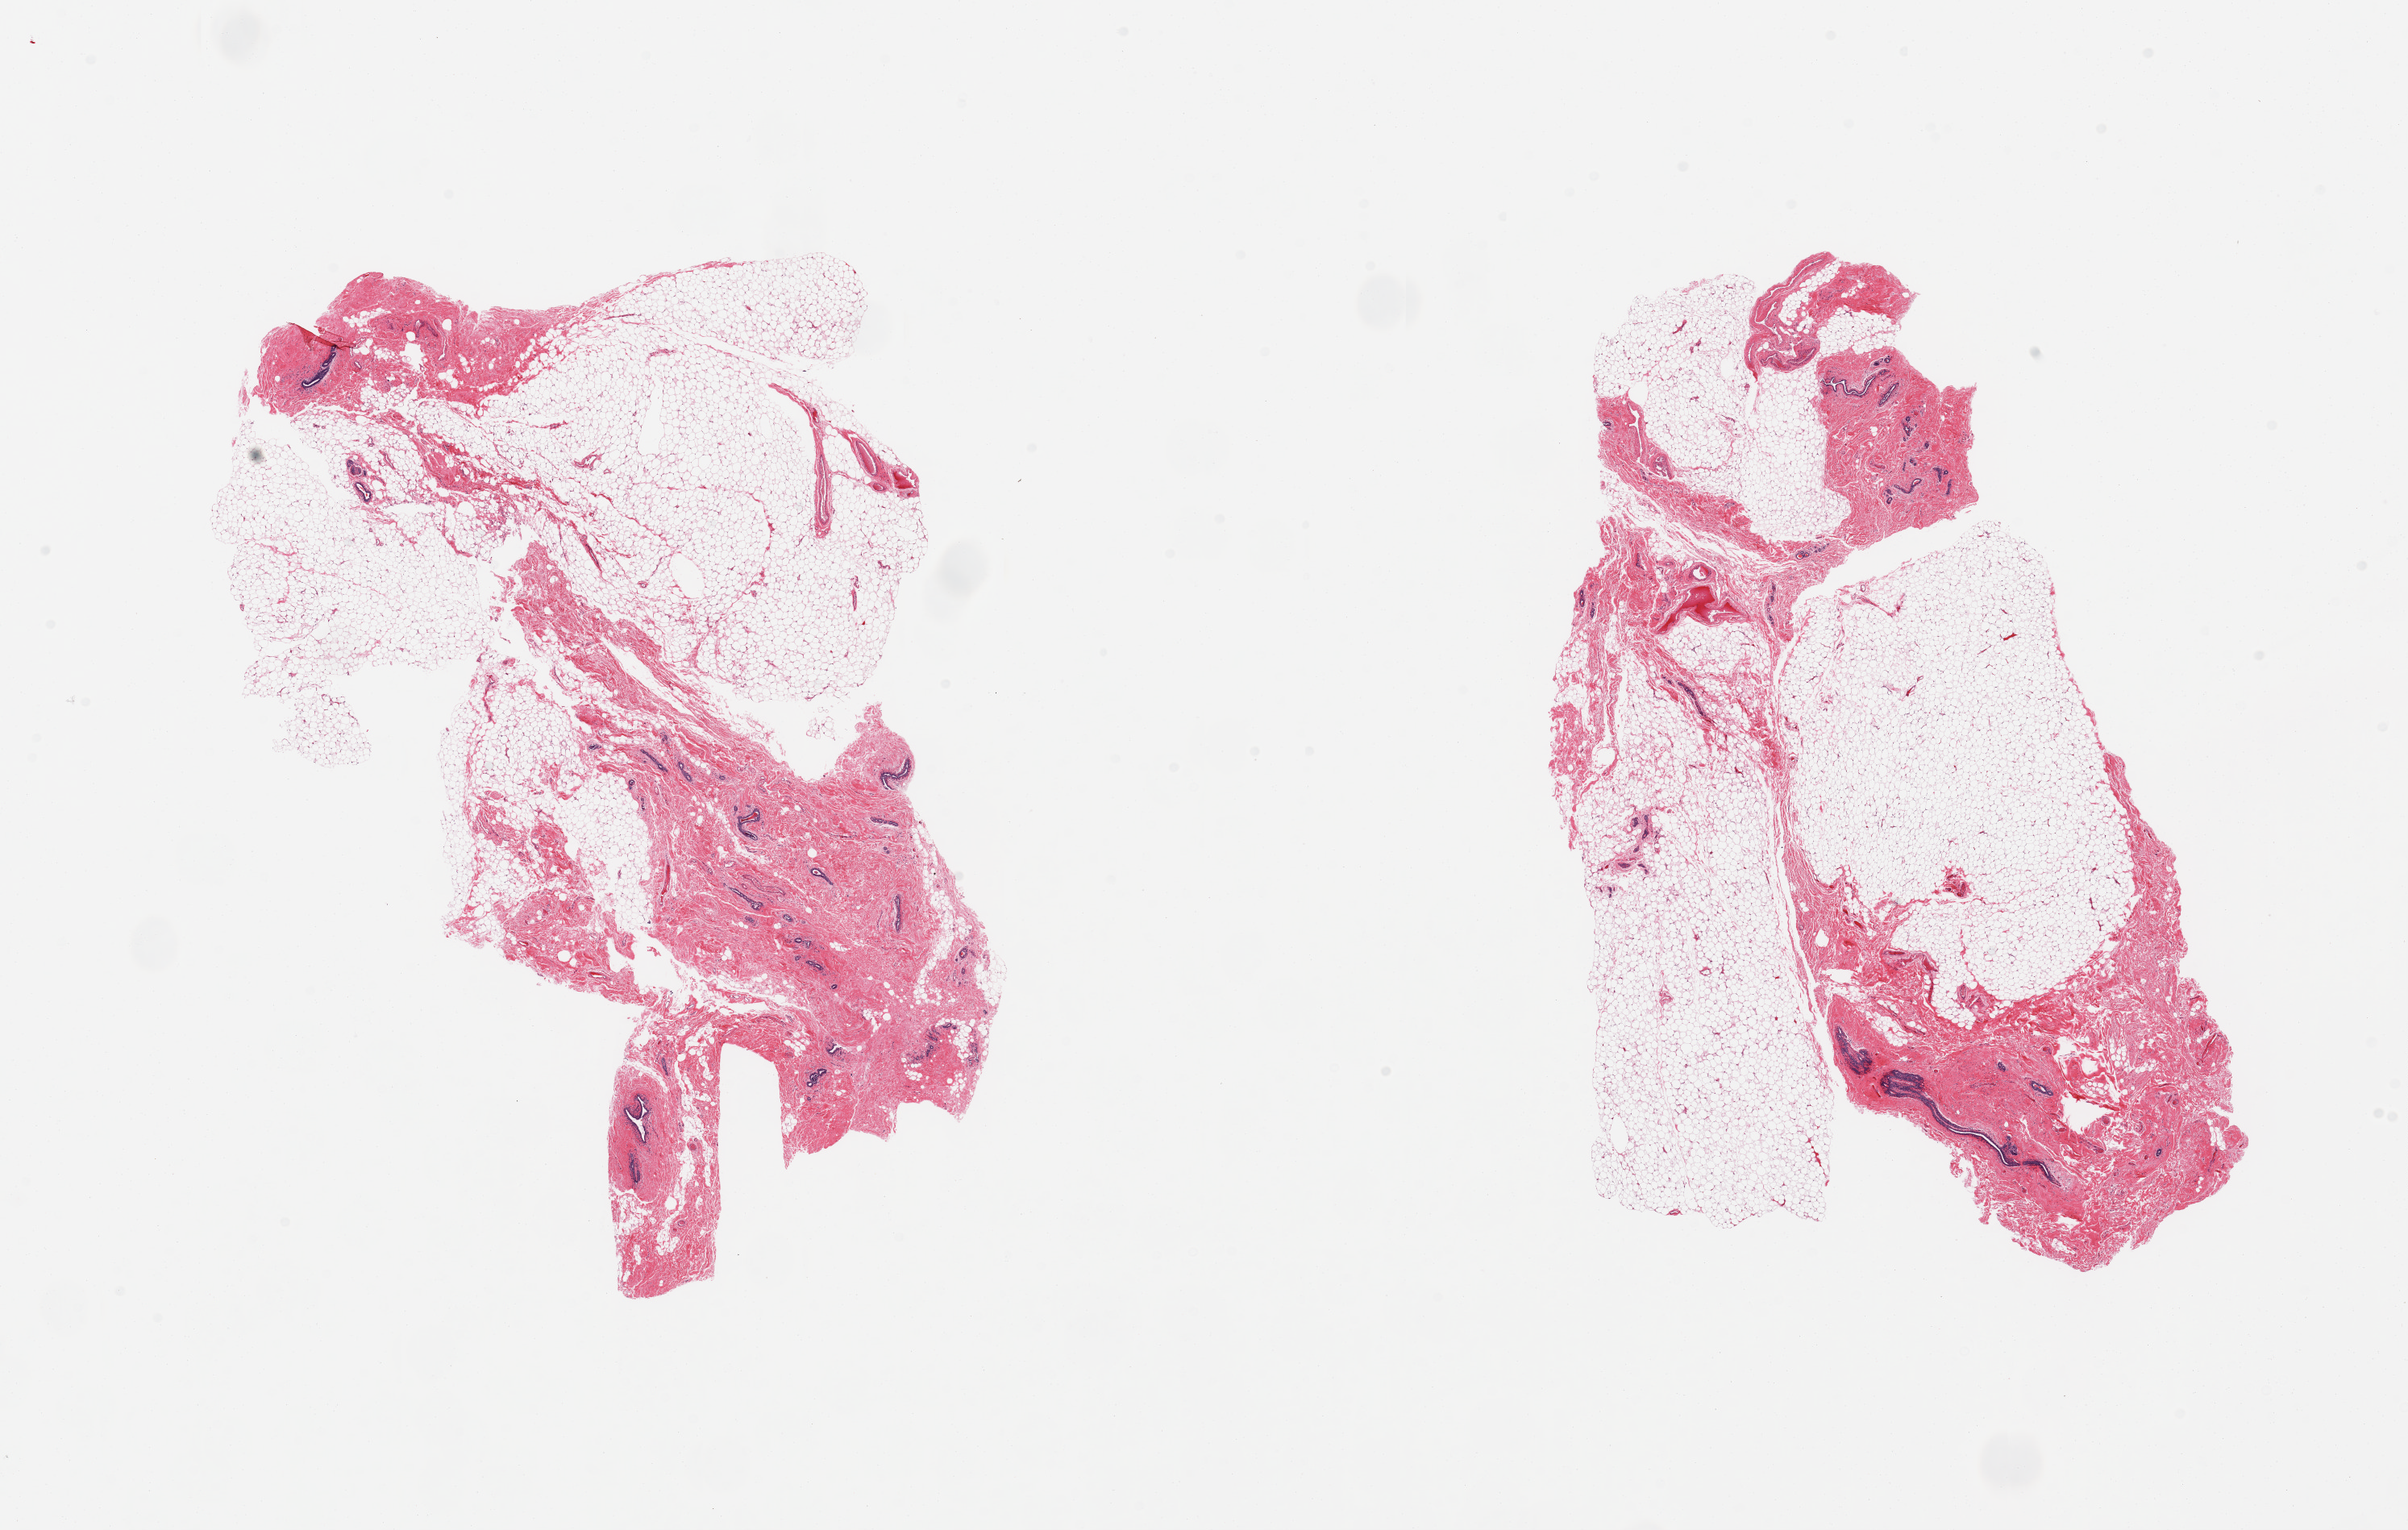
Haematoxylin and eosin whole-slide image, brightfield — a low-resolution overview of the entire scanned area, about 23.6 x 15.0 mm (acquisition: 20x scan); PAXgene-fixed paraffin-embedded (PFPE) section; target tissue: breast; donor tissue sample. Donor sex: female.
* pathologist's review note for this sample: 2 pieces, ductal elements